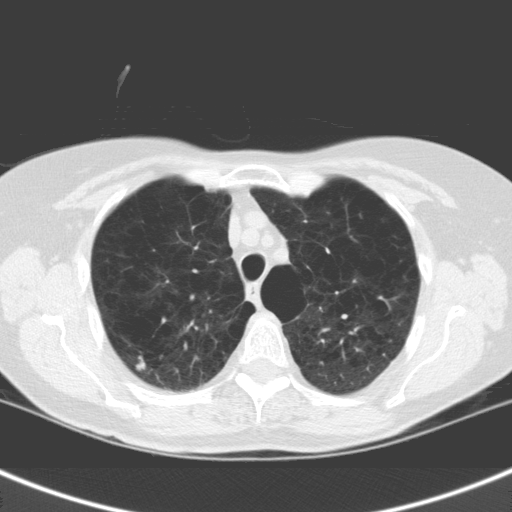
Low-dose screening chest CT, one axial slice; slice 120 of 158 in the series (ordered by position); lung window (W 1500 / L -600 HU); 3.2 mm slice thickness; 512 × 512 image matrix, field of view 301 × 301 mm.
Structures marked on this image (manually delineated by an expert):
- lesion 1 (tumor, upper lobe of right lung): bounding box (x1, y1, x2, y2) in pixels: (136, 362, 146, 371)